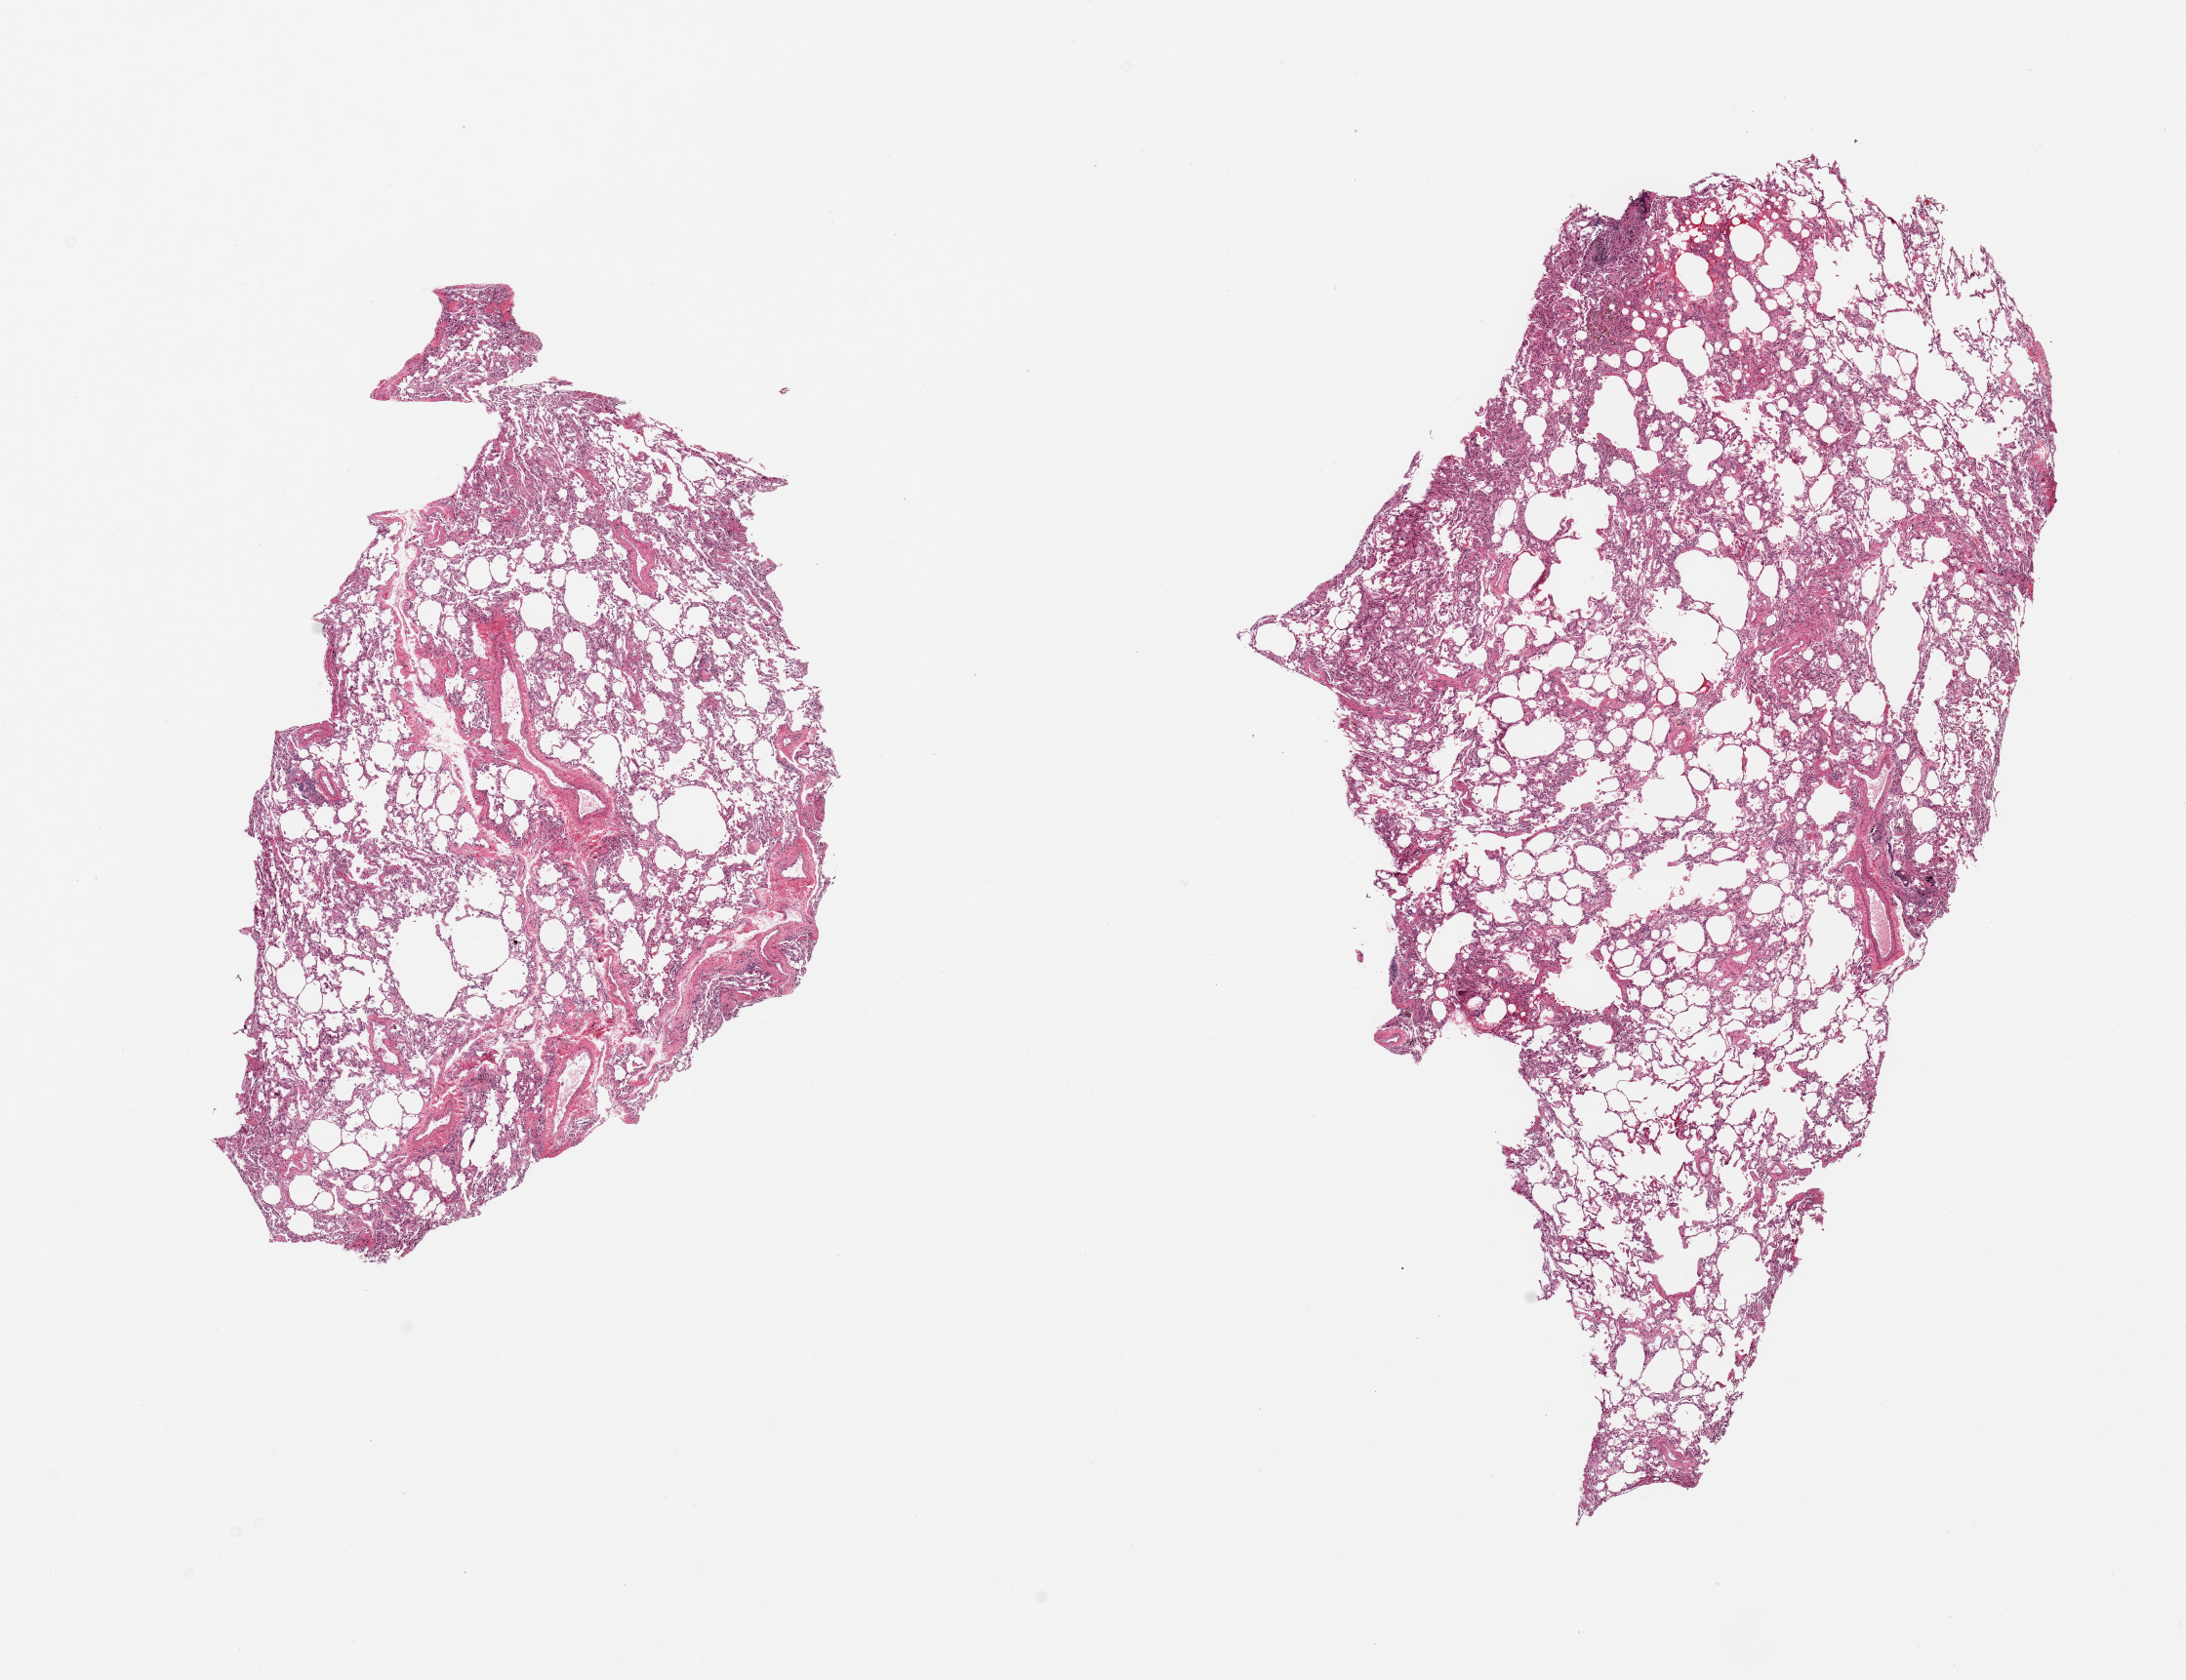
Digitized haematoxylin and eosin-stained section — a low-resolution overview of the entire scanned area, about 17.7 x 13.6 mm (acquisition: 20x scan), PAXgene-fixed paraffin-embedded (PFPE) section, target tissue: lung, donor tissue sample.
Reviewer comment on this tissue sample: 2 pieces, modeate emphysematous features, minimal congestion.